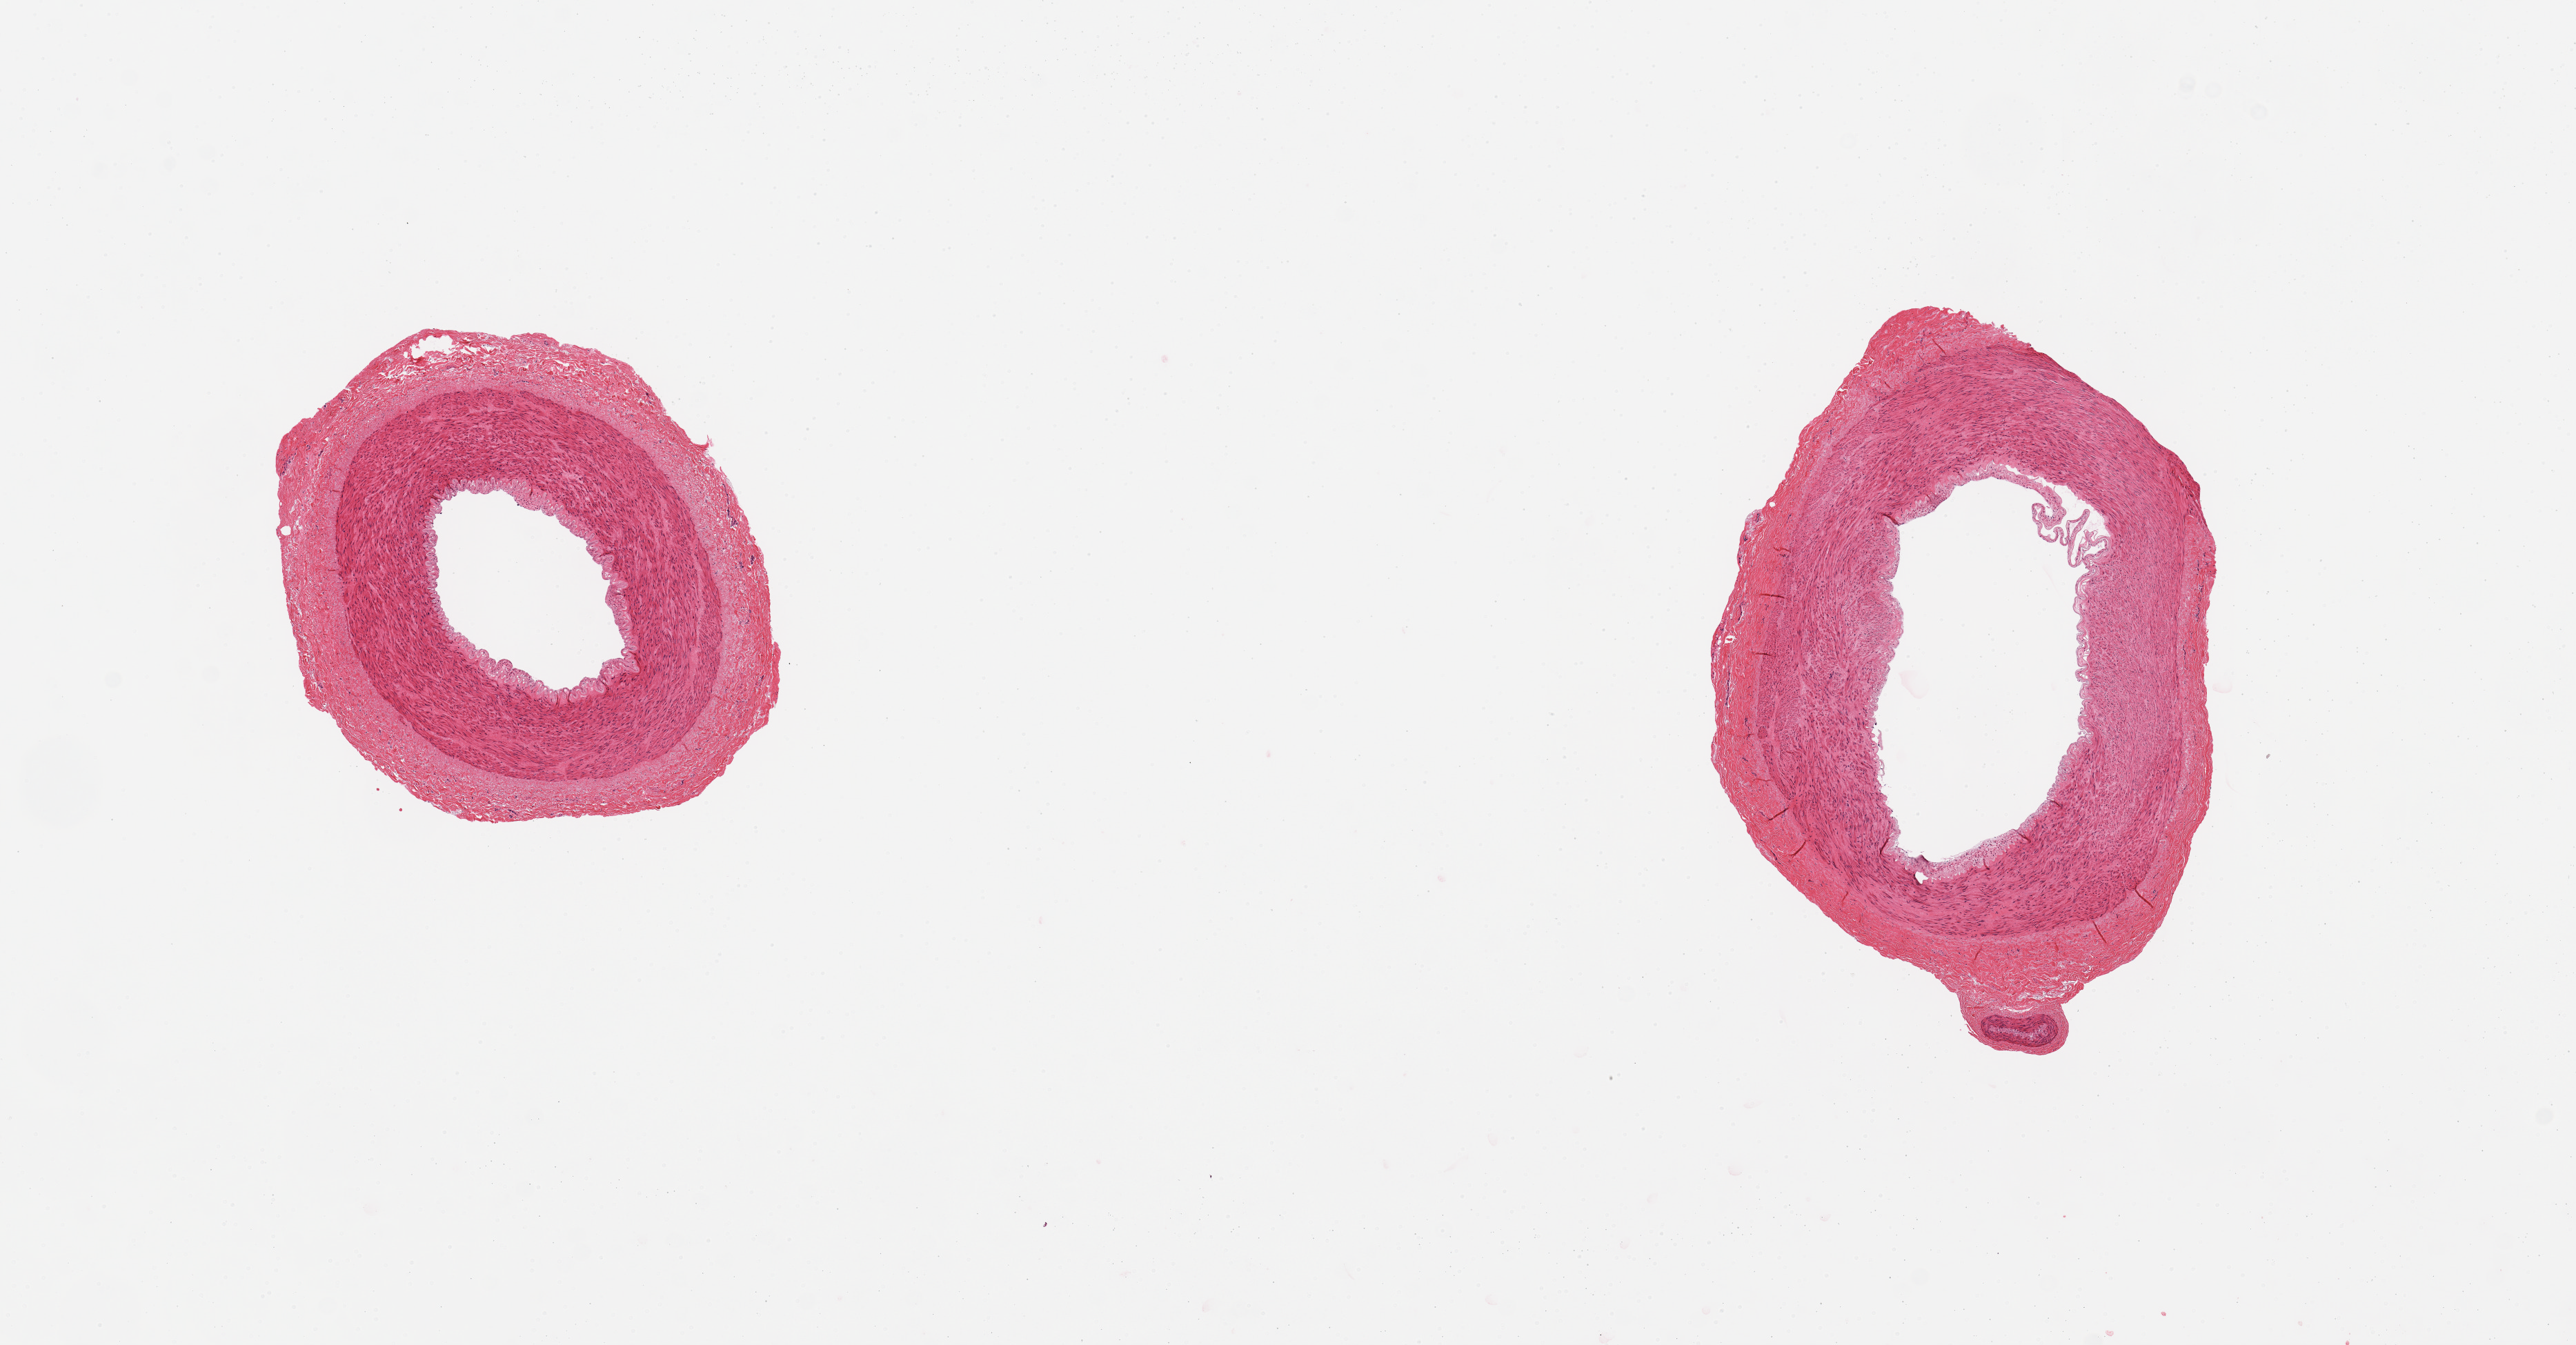
Digitized H&E-stained section — shown as a low-resolution overview of the whole scanned area (about 14.8 x 7.7 mm, from a 20x scan). PAXgene-fixed paraffin-embedded (PFPE) section. Target tissue: tibial artery. Tissue donor sample. Donor: female.
- review note (as recorded): 2 pieces, clean specimens